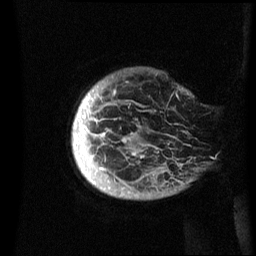
Breast MRI (dynamic contrast-enhanced), one sagittal slice; slice 2 of 60 in the series (ordered by position); dynamic contrast-enhanced series, image 2 of 3 at this slice position (ordered by acquisition); 1.5 T; TE 4.2 ms, TR 8.4 ms; 256 × 256 image matrix, field of view 230 × 230 mm. Female patient, age 48 years.
Annotated regions visible in this slice (semi-automatically segmented with operator editing):
- analysis volume of interest (the breast-tissue region the enhancement analysis was run in; not a lesion): bounding box <72,68,201,200> (left, top, right, bottom; pixels)
- tumour enhancement mask (voxels above the 70 % enhancement threshold inside the analysis volume of interest): <73,91,126,171>